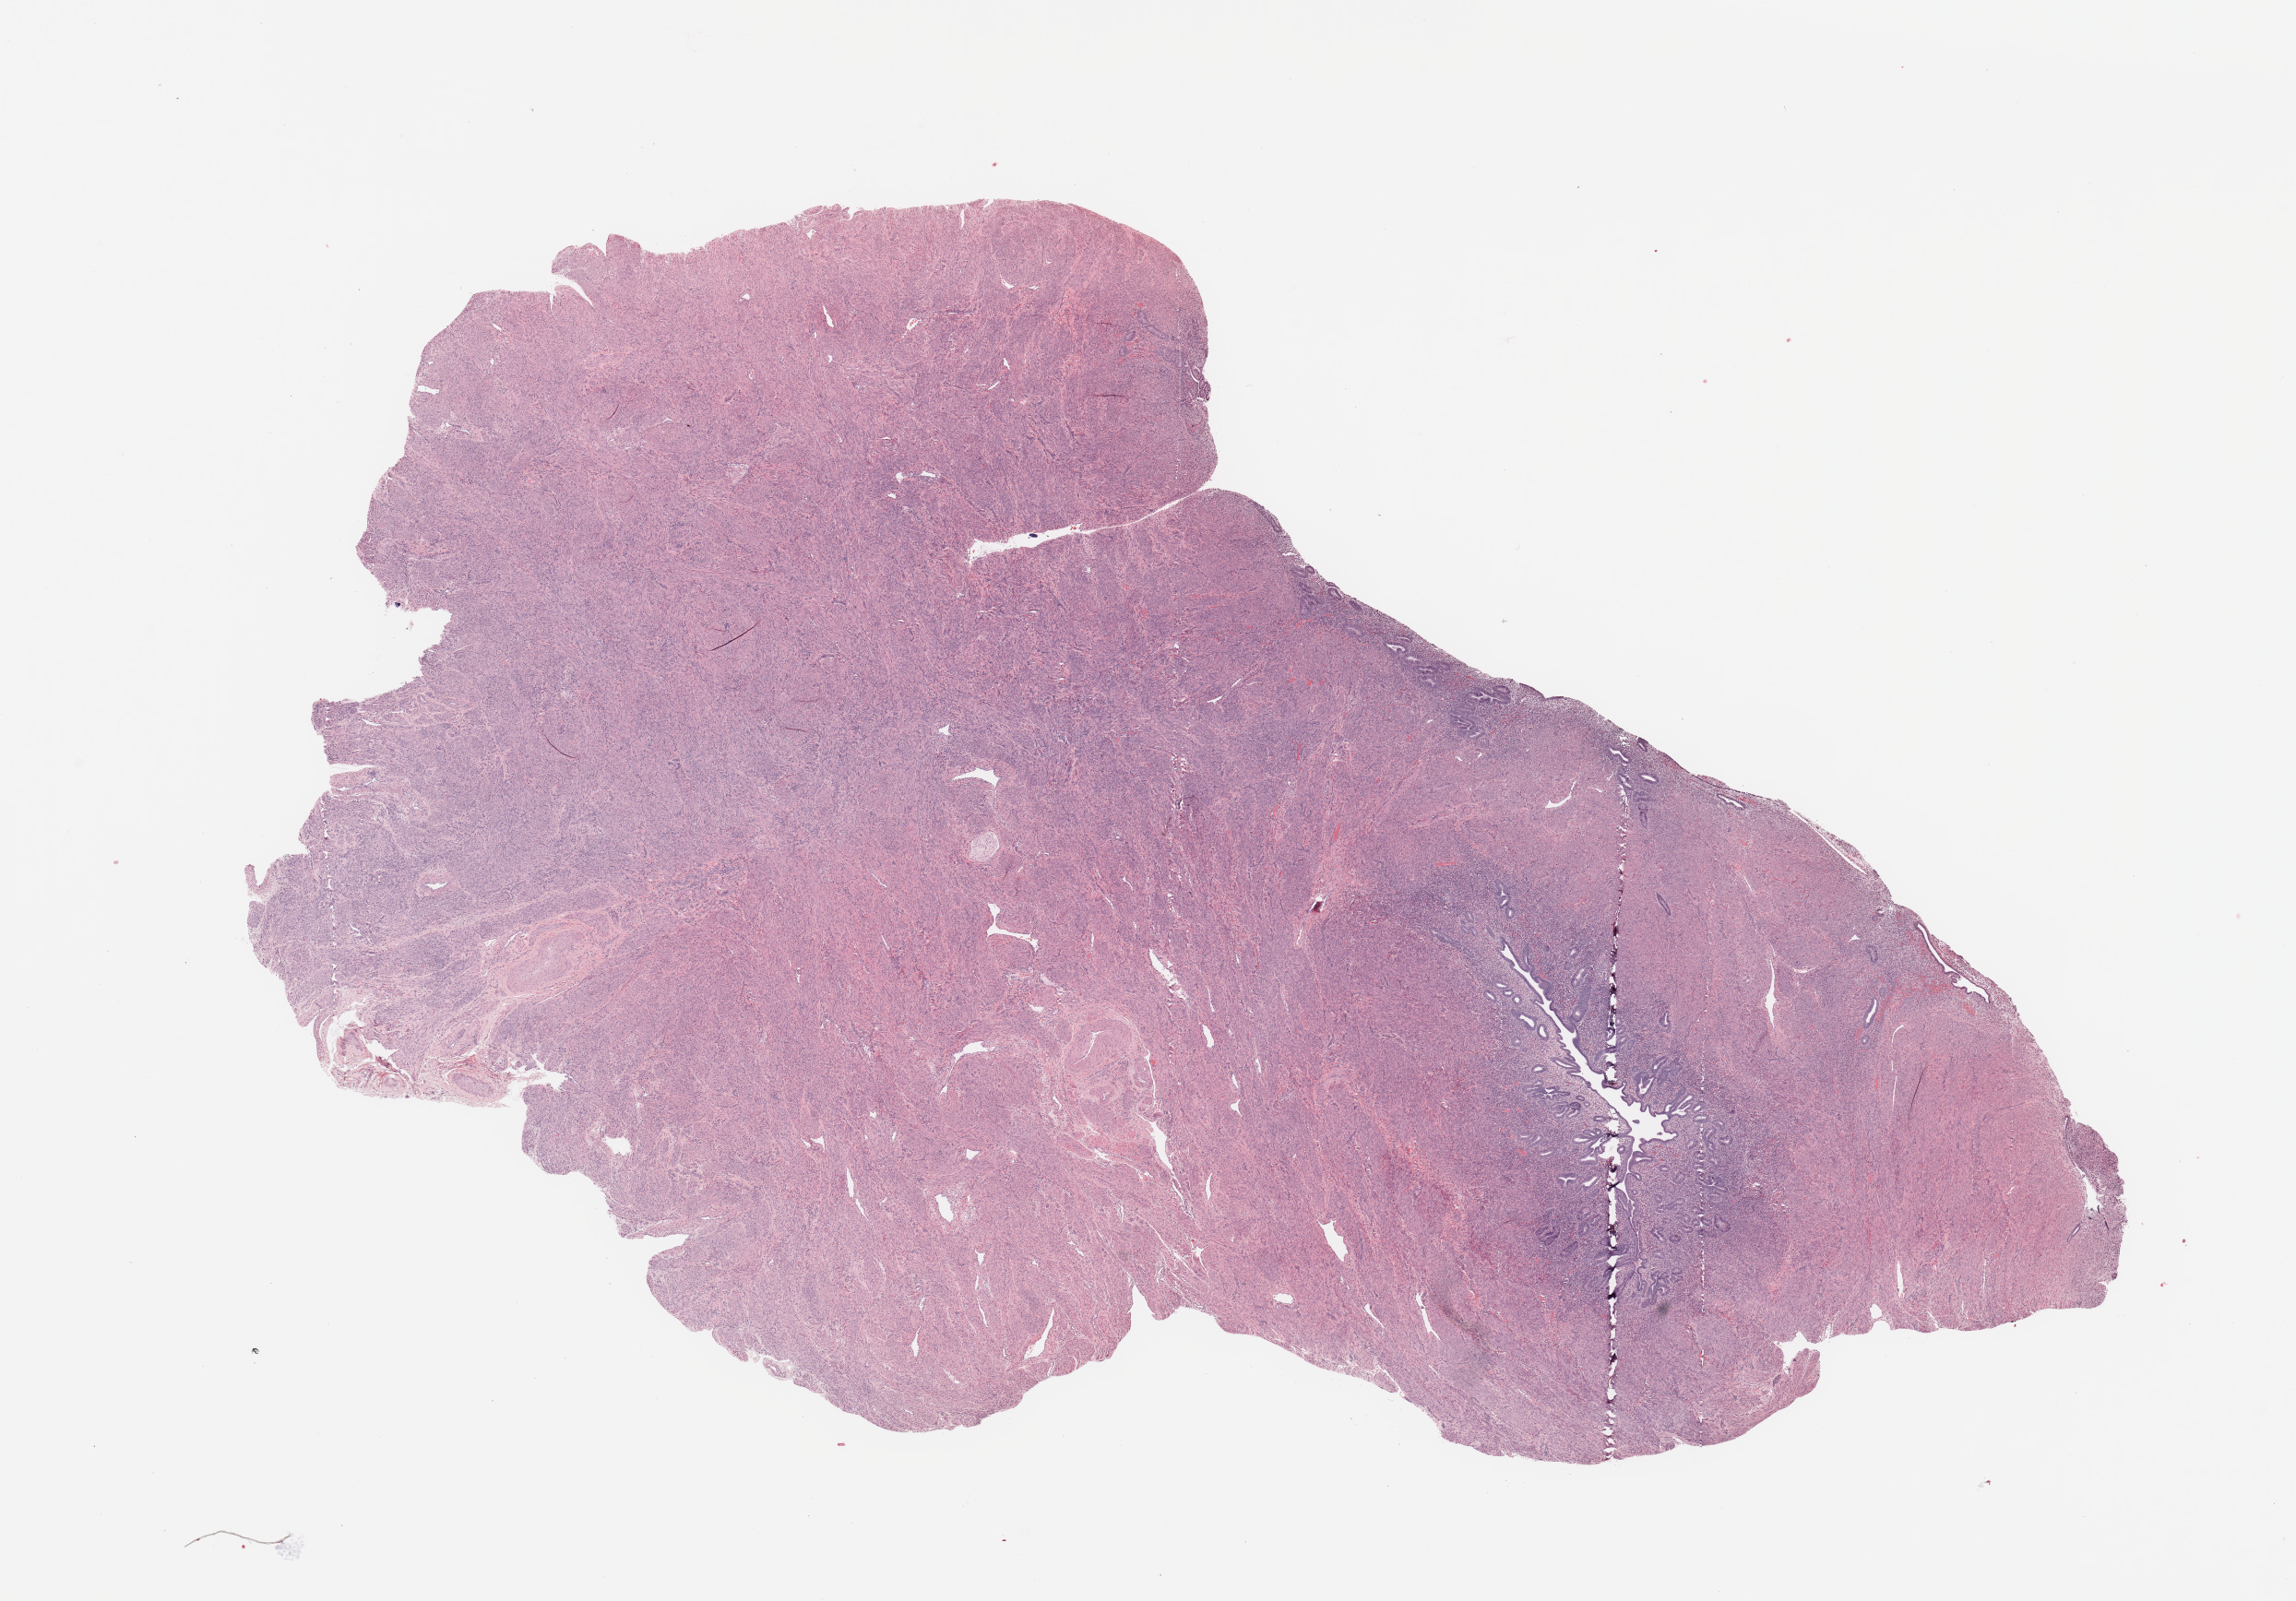
Whole-slide histology image, H&E-stained — low-resolution overview of the scanned area, about 19.7 x 13.7 mm; normal (non-tumour) tissue sample, uterus. Patient: female, age 54 years.
- this section: normal (non-tumour) tissue from the same patient
- patient diagnosis: Endometrioid adenocarcinoma, NOS